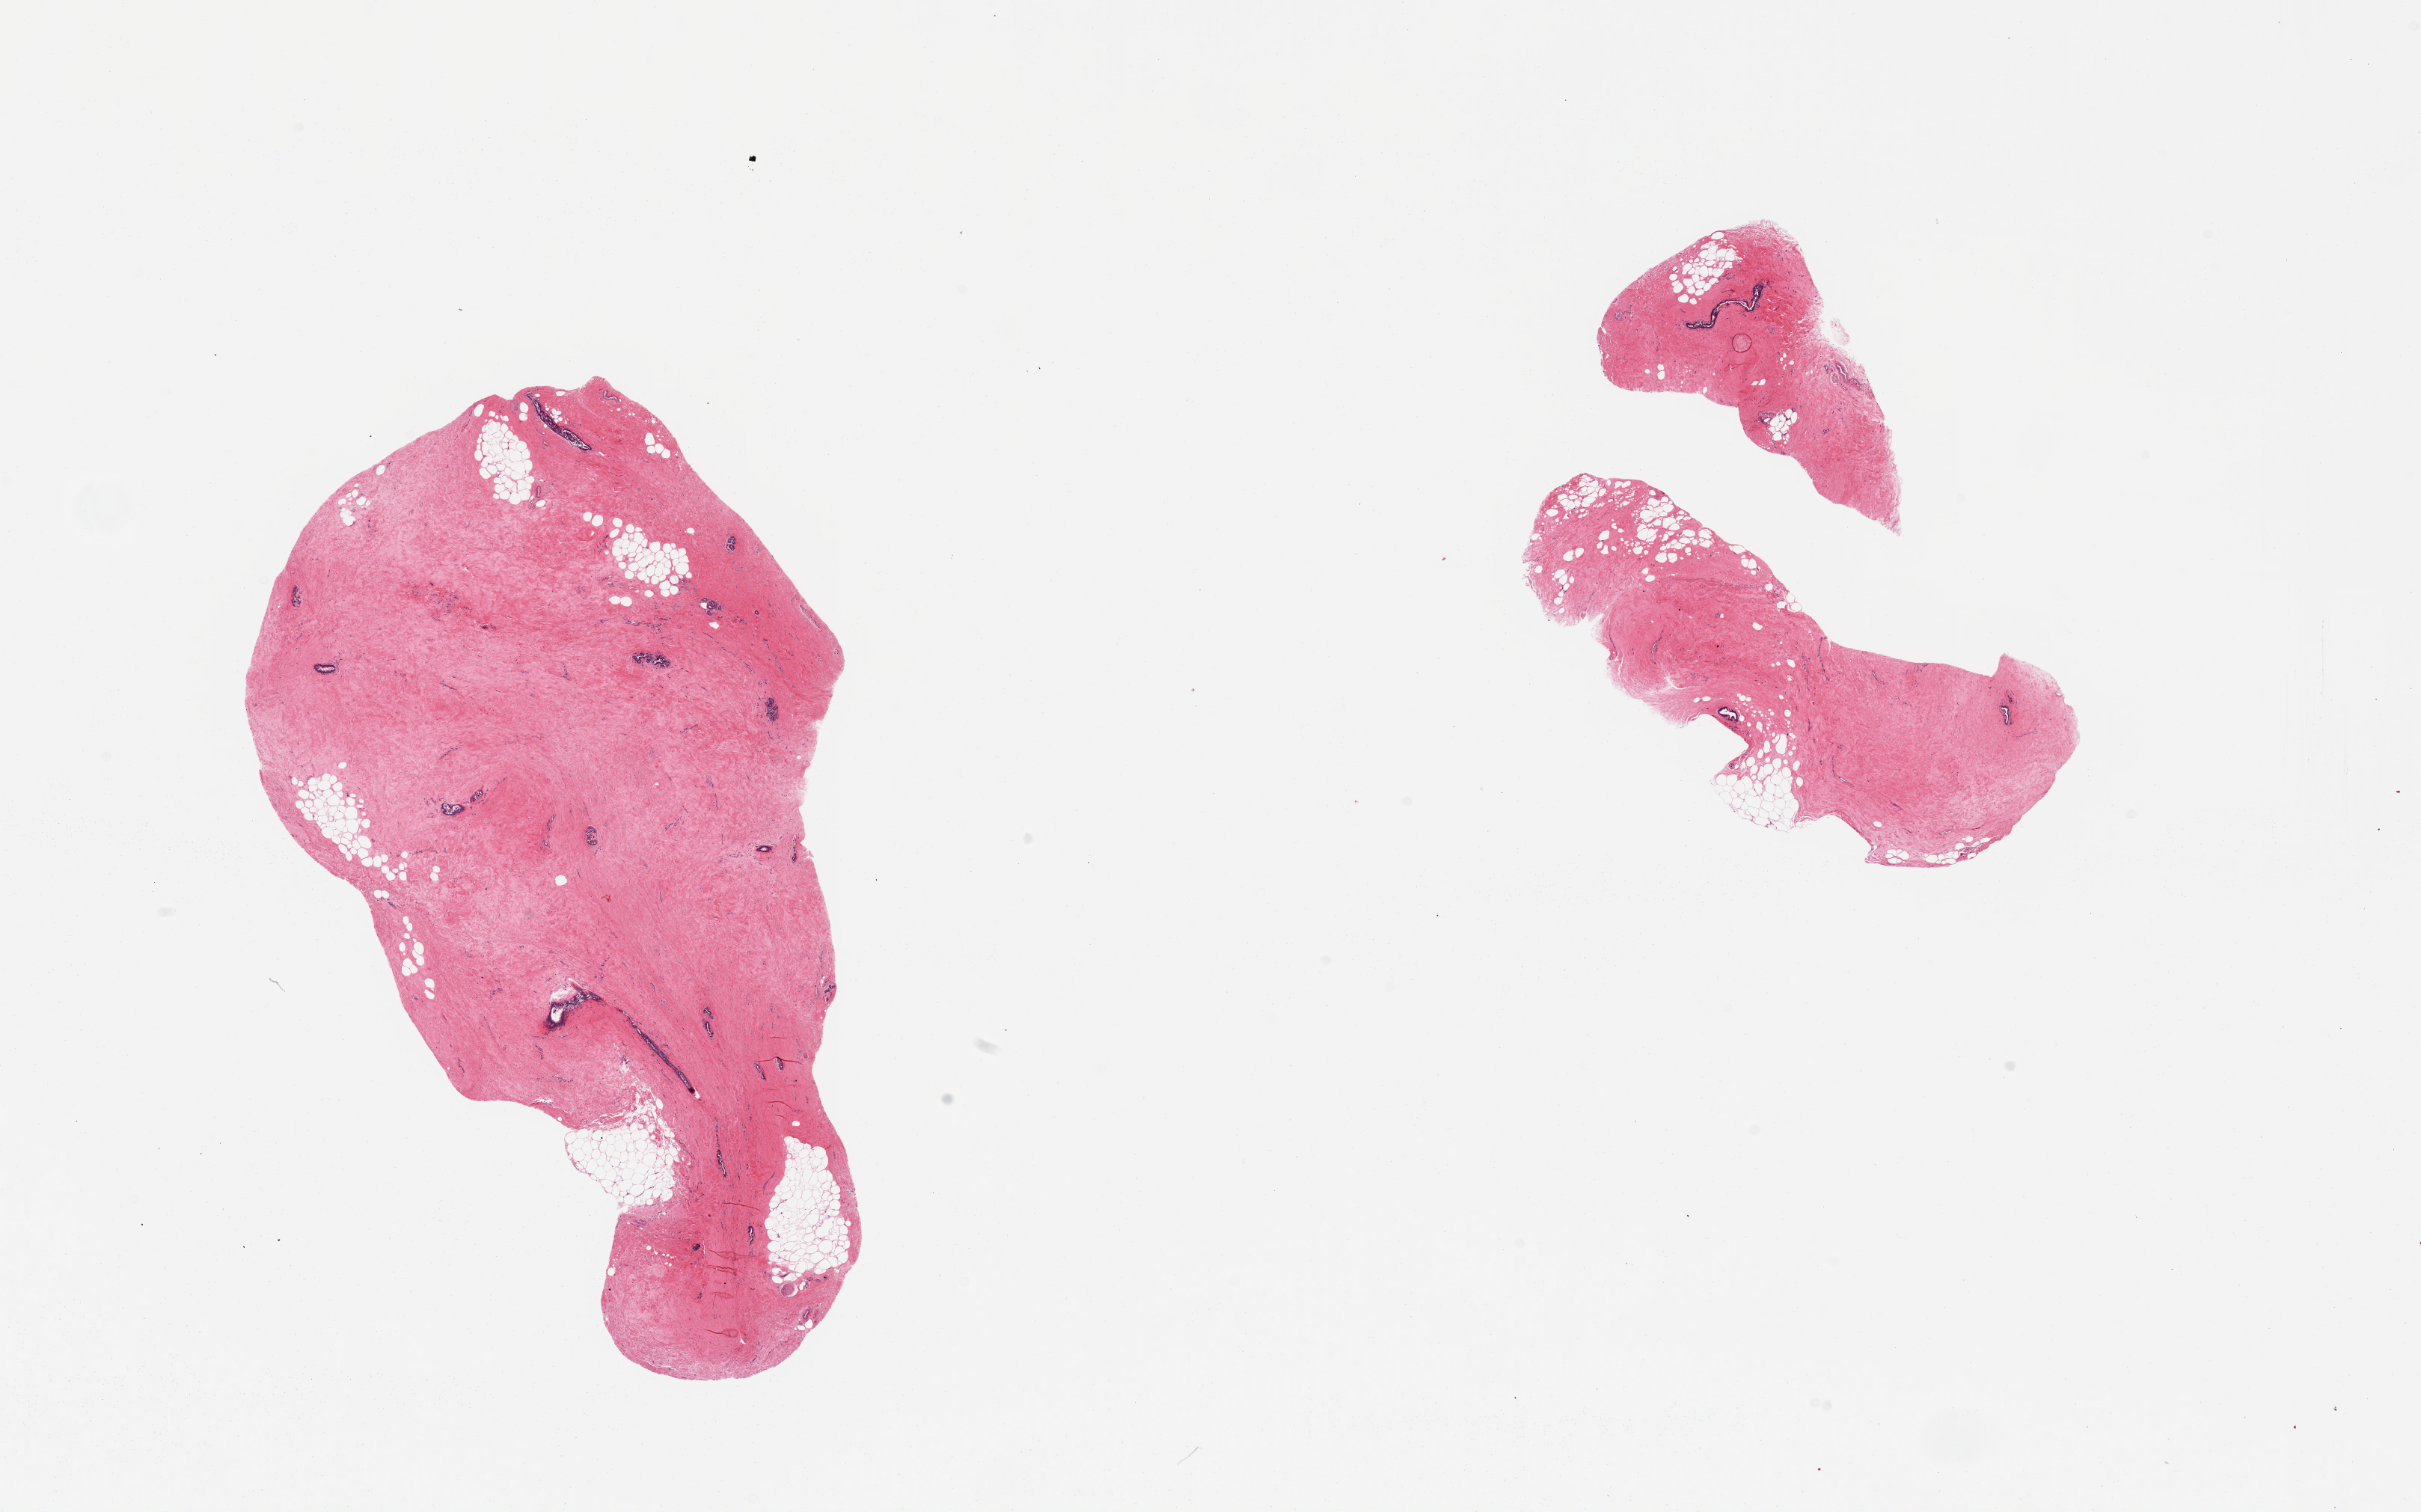
Whole-slide image, haematoxylin and eosin stain, shown as a low-resolution overview of the whole scanned area (about 25.6 x 16.0 mm, slide scanned at 20x), PAXgene-fixed paraffin-embedded (PFPE) section, section of breast (target tissue), donor tissue sample. Donor sex: male.
* pathologist's review note for this sample: 2 pieces; gynecomastoid hyperplasia